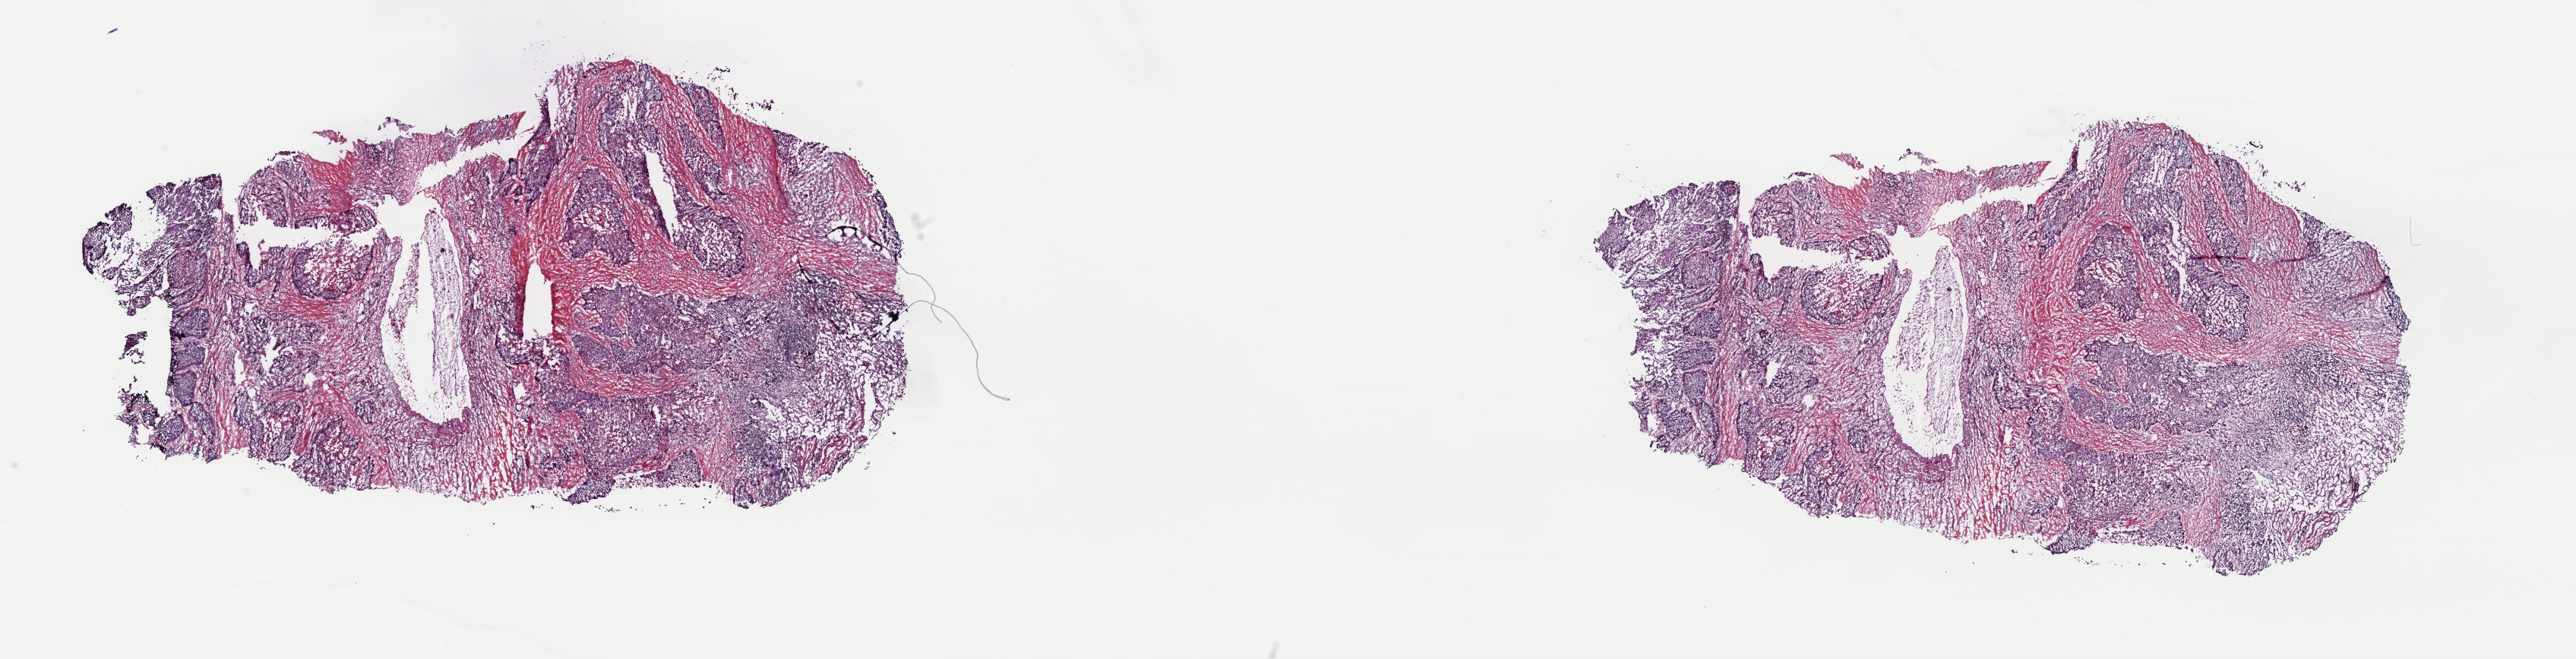
Digitized Hematoxylin and eosin (H&E) stained tissue section (whole slide), shown as a low-resolution overview of the whole scanned area (about 26.8 x 6.9 mm); frozen section from the top of the tissue portion; primary tumour sample from the lung. Male patient; age at initial diagnosis 70 years. Pathologist review of this section (percent, as recorded): tumour cells 95%, tumour nuclei 70%.
Diagnosis: Squamous cell carcinoma, keratinizing, NOS (middle lobe, lung).